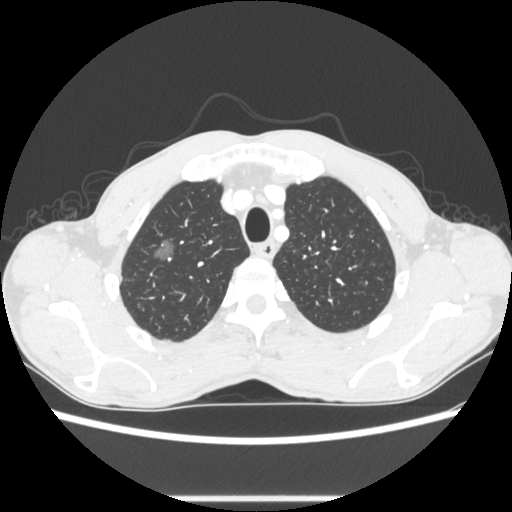
Chest CT, one axial slice; position 236 of 289 along the scan axis; reconstruction kernel STANDARD; lung window (W 1500 / L -600 HU); 1.25 mm slice thickness; 512 × 512 image matrix. Patient: male, 54 years. Case-level facts recorded for this patient, not image findings: clinical TNM (as recorded): T1a N0 M0.
Annotated regions visible in this slice (rectangle marked by the reading radiologist):
- lung tumour (recorded histology: adenocarcinoma): bounding box [x1, y1, x2, y2] px = [148, 232, 184, 265]